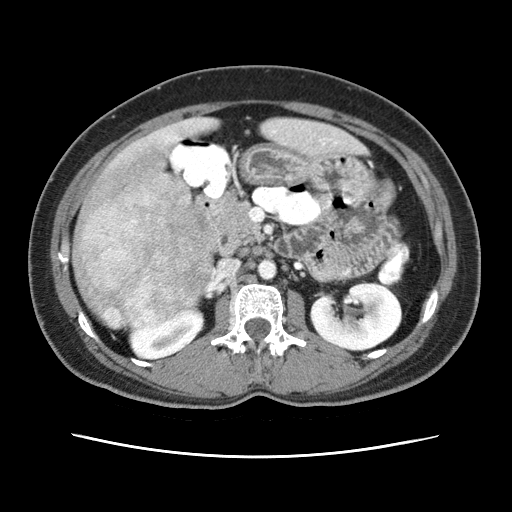
Contrast-enhanced abdominal CT (liver protocol), one axial slice; position 16 of 79 along the scan axis; reconstruction kernel STANDARD; soft-tissue window (W 400 / L 40 HU); 2.5 mm slice thickness; 512 × 512 image matrix, field of view 340 × 340 mm. Case-level facts recorded for this patient, not image findings: diagnosis: hepatocellular carcinoma (patient treated with transarterial chemoembolisation; whether this scan precedes or follows treatment is not stated here); TNM stage (as recorded): Stage-I; Child-Pugh class: A.
Annotated regions visible in this slice (semi-automatically segmented with operator editing):
- abdominal aorta: bounding box [x1, y1, x2, y2] px = [258, 258, 277, 277]
- liver parenchyma outside the tumour (the mass and vessels are separate outlines, so this box may not span the whole liver): [74, 117, 365, 328]
- mass: [74, 150, 213, 325]
- liver vessels: [174, 131, 275, 139]